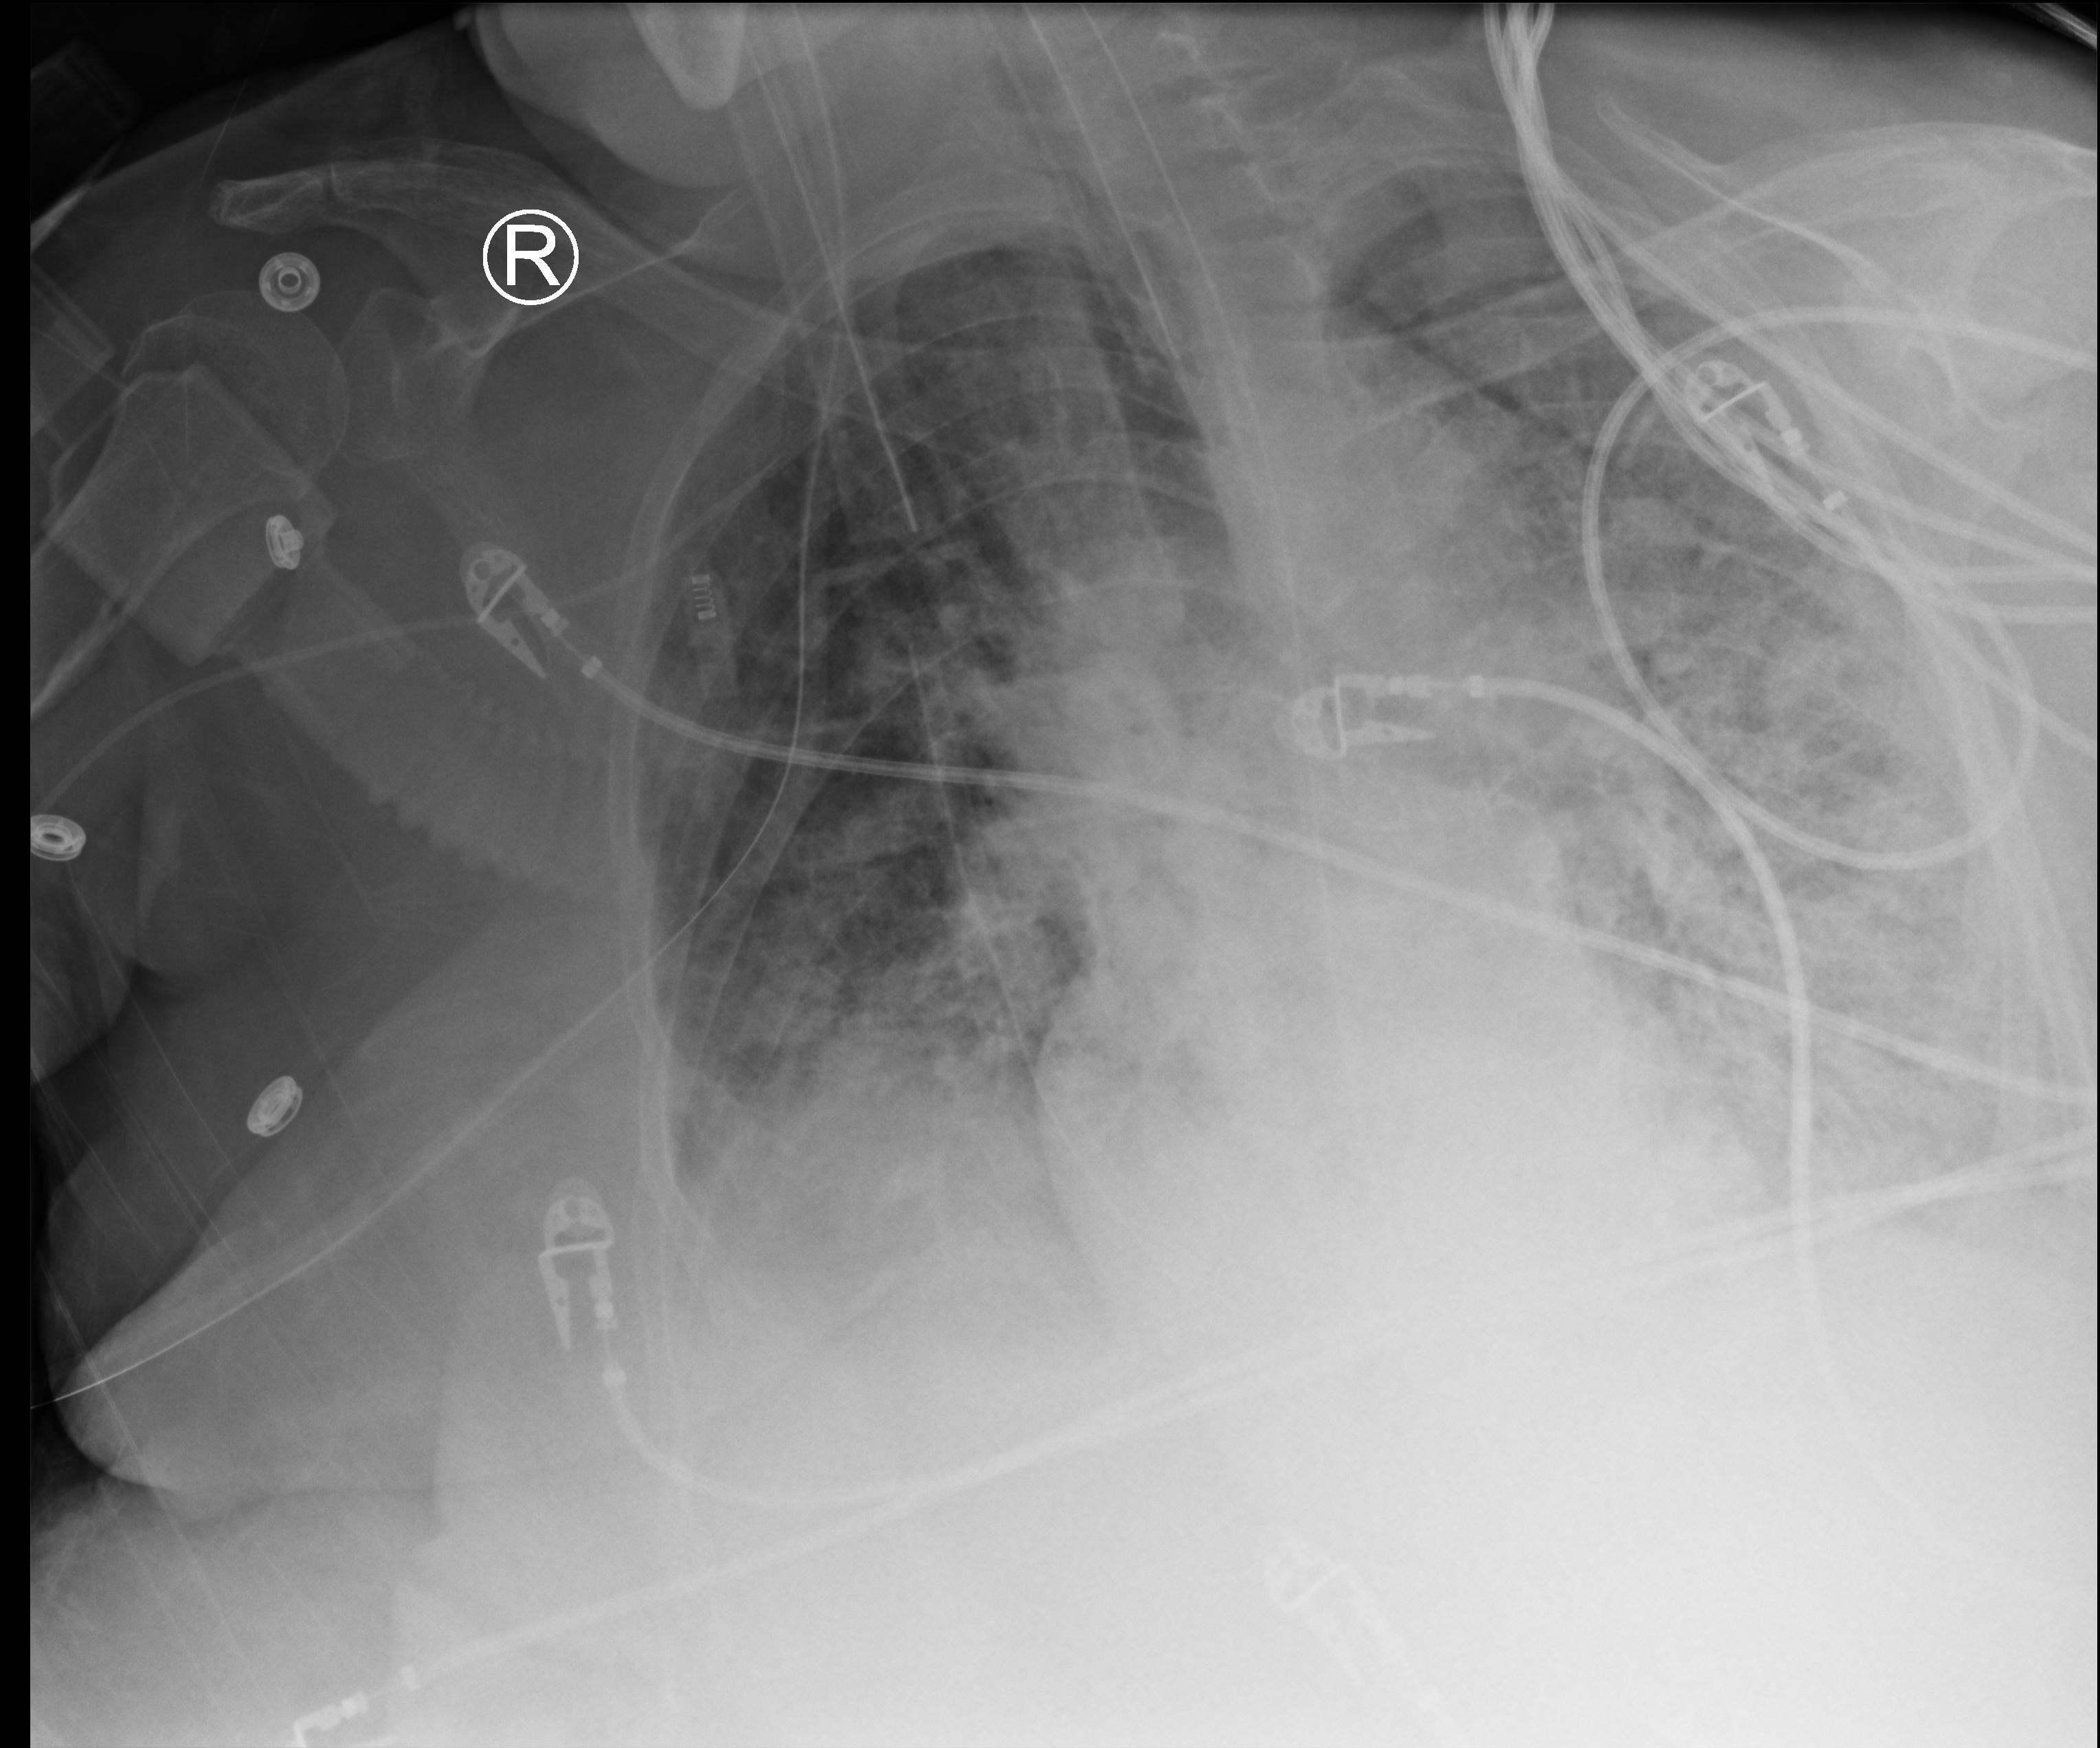
Bedside chest radiograph (computed radiography); anteroposterior (AP) projection. Female patient hospitalised with COVID-19, age 60–74 years.
From the hospital-stay record, not from the radiograph (when in the stay this image was taken is not recorded): length of hospital stay: 15 days; chronic kidney disease (admission record): no; admitted to intensive care during this hospital stay: yes.